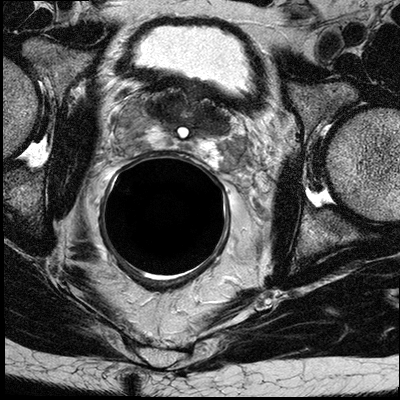
MRI of the prostate; 3 images, each a single mid-volume slice chosen by position (not for content).
Image 1: T2-weighted axial slice, series "T2W_TSE_AX", slice 17 of 32.
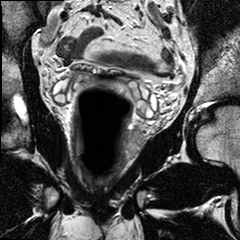
Image 2: T2-weighted coronal slice, slice 13 of 24.
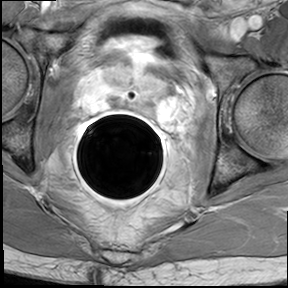
Image 3: axial dynamic contrast-enhanced (DCE) T1-weighted image, series "AX BLISS_GAD_8", slice 17 of 32, dynamic phase 5 of 8, 6 mm slice thickness.
Report of this MRI examination:
FINDINGS: The zonal anatomy is preserved. In the left lateral and posterio-lateral peripheral zone from 2-6 o'clock and the adjacent central gland of the prostate base, mid third, and extending into the apical third, there is a large geographic T2 hypointense area seen, with highly suspicious kinetics on the DCE series. Maximal extension of the dominant mass is 3.1 x 1.5 x 2.4 cm; in the mid 3rd of the prostate the tumor crosses the midline and involves also the posterior lateral upper right peripheral zone. (till 7 o'clock). At the mid third level the prostate capsule is interrupted at 5 o'clock; in in the apex of between 4 and 5 o'clock the gland border is regular or indistinct; in addition there is suspicious enhancement seen beyond the prostate capsule in the mid-third of the prostate between 3 o'clock and 5 o'clock which is suggestive for extracapsular disease (towards the left neurovascular bundle)In addition, there is also T2-hypointense signal seen beyond the capsule with maximal radial extension of 3-4 mm (towards the left neurovascular bundle). The right neurovascular bundle is uninvolved. The seminal vesicles are unremarkable. No suspicious the enlarged obturator and iliac lymph nodes on either side. IMPRESSION: Large predominantly left sided prostate tumor within the left lateral and posterior lateral peripheral zone with involvement of the adjacent central gland; and crossing the midline into the right peripheral zone. Findings are highly suggestive of extracapsular extension on the left, posterior-lateral towards the left neurovascular bundle; No involvement of the right neurovascular bundle; no seminal vesicles infiltration; no pelvic lymphadenopathy. Smaller suspicious areas are also seen in the left in the right peripheral zone between 9 and 8 o'clock; with suspicious enhancement along the capsule towards the right neurovascular bundle. Beginning extracapsular disease on the right side, lateral peripheral zone cannot be excluded. Final impression: Extensive bilateral tumor, most likely with extracapsular extension on the left and possible extracapsular extension on the right. No evidence of seminal vesicle infiltration; no pelvic lymphadenopathy.